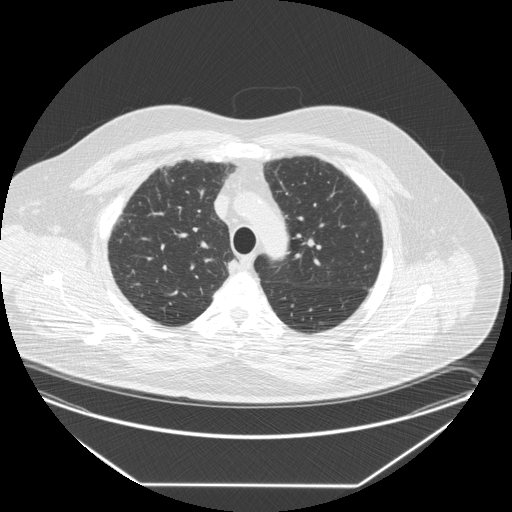
Low-dose screening chest CT, one axial slice; reconstruction kernel STANDARD; 120 kVp; lung window (W 1500 / L -600 HU); 512 × 512 image matrix.
Annotated regions visible in this slice (outlined manually by an expert reader):
- lesion 1 (tumor, upper lobe of right lung): bounding box [x1, y1, x2, y2] px = [228, 259, 239, 274]